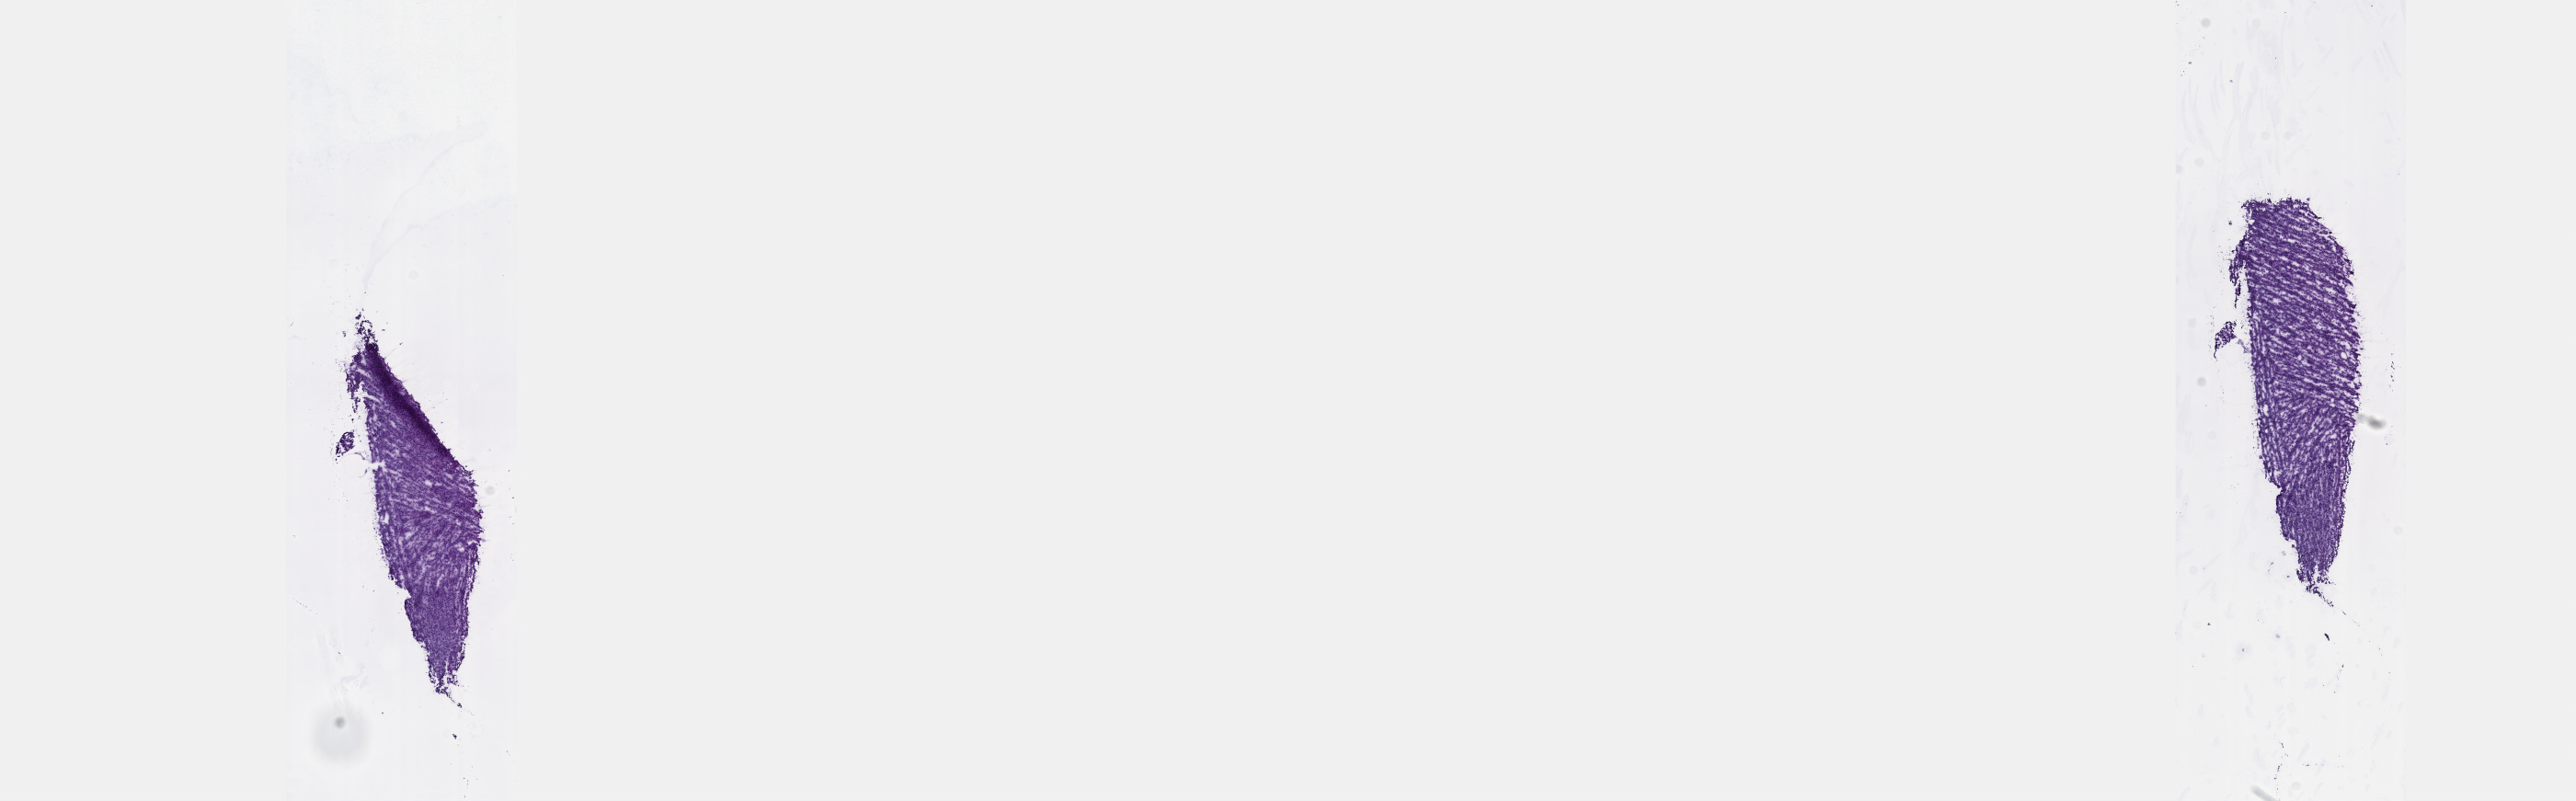
Digitized Hematoxylin and eosin (H&E) stained tissue section (whole slide) — shown as a low-resolution overview of the whole scanned area (about 22.6 x 7.0 mm). Frozen section. Sample: primary tumour, uvea. Patient: female, age at initial diagnosis 57 years. Composition of this section per pathologist review: tumour cells 100%, tumour nuclei 95%, normal cells 0%, stromal cells 0%, necrosis 0%. Inflammatory infiltration, as recorded: lymphocyte infiltration 0%, monocyte infiltration 0%, neutrophil infiltration 0%.
• AJCC pathologic stage: IIA (7th edition)
• histologic diagnosis: Spindle cell melanoma, NOS
• laterality: left